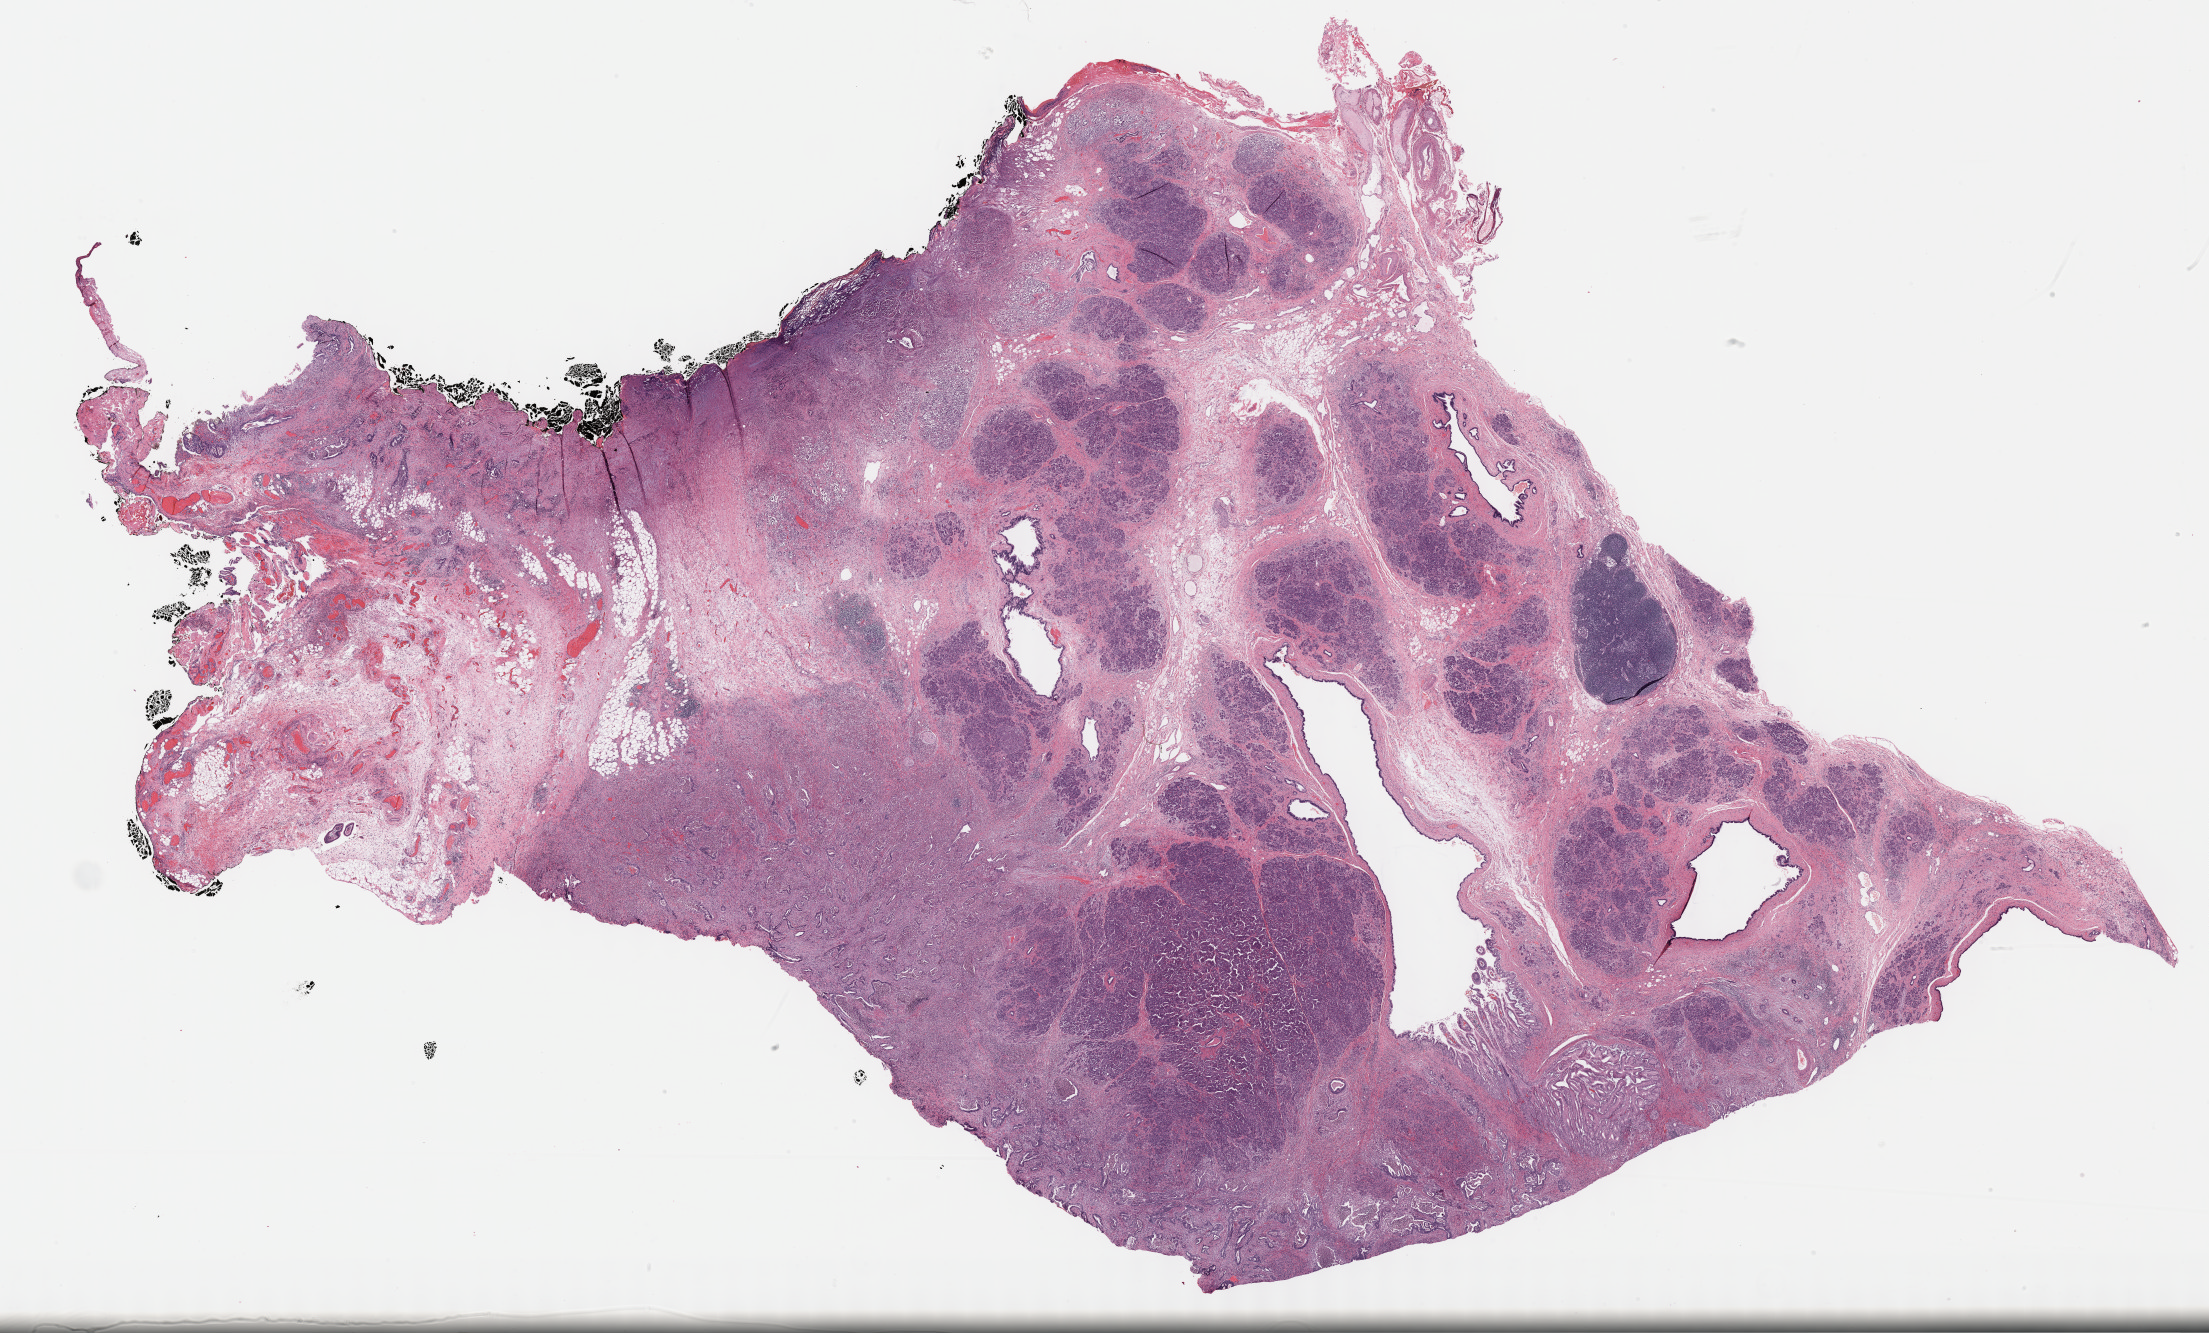
Hematoxylin and eosin (H&E) stained whole-slide image, a low-resolution overview of the entire scanned area, about 35.7 x 21.6 mm; formalin-fixed paraffin-embedded (FFPE) diagnostic section; pancreas, primary tumour sample. Patient: female, age at initial diagnosis 65 years. Histologic grade: G2 (moderately differentiated).
AJCC pathologic stage: IV (7th edition). Histologic diagnosis: Infiltrating duct carcinoma, NOS. Lymph nodes positive (case pathology): 3 of 8 examined.